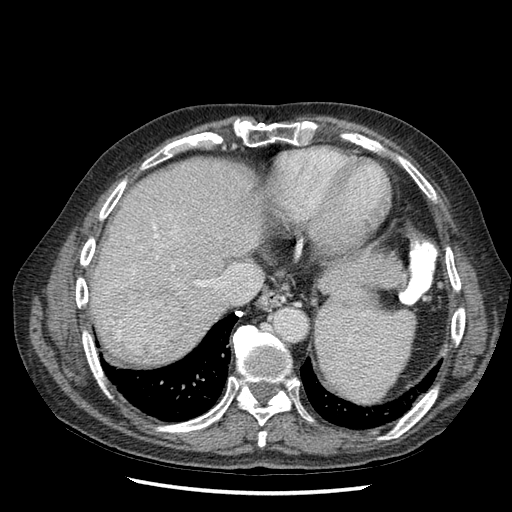
Contrast-enhanced abdominal CT (liver protocol), one axial slice. Slice 56 of 67 in the series (ordered by position). Reconstruction kernel STANDARD. Soft-tissue window (W 400 / L 40 HU). 2.5 mm slice thickness. 512 × 512 image matrix, field of view 360 × 360 mm. From the clinical record (not read from this slice): diagnosis: hepatocellular carcinoma (patient treated with transarterial chemoembolisation; whether this scan precedes or follows treatment is not stated here); TNM stage (as recorded): Stage-I; Child-Pugh class: A; tumour differentiation: moderately differentiated.
Outlined on this slice (semi-automatic segmentation, software-assisted and operator-edited):
- abdominal aorta: box from (x=275, y=307) to (x=308, y=339) px
- liver parenchyma outside the tumour (the mass and vessels are separate outlines, so this box may not span the whole liver): (x=90, y=156)–(x=269, y=362)
- mass: (x=106, y=282)–(x=181, y=353)
- liver vessels: (x=132, y=234)–(x=186, y=274)